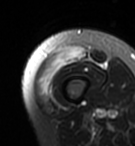
MRI of an extremity soft-tissue mass, one axial slice. Slice 8 of 95 in the series (ordered by position). T2-weighted fat-saturated. MR volume resampled by the dataset authors to the PET/CT grid (not the native acquisition matrix). 3.27 mm slice thickness. 135 × 146 image matrix, field of view 132 × 143 mm. Female patient. From the clinical record (not read from this slice): histological type: pleiomorphic undifferentiated sarcoma; grade: high; site of the primary tumour: right quadricep.
Structures marked on this image (expert contour drawn on MRI and transferred to this co-registered scan by the dataset authors):
- gross tumour volume including surrounding oedema: bounding box [x1, y1, x2, y2] px = [37, 47, 86, 99]